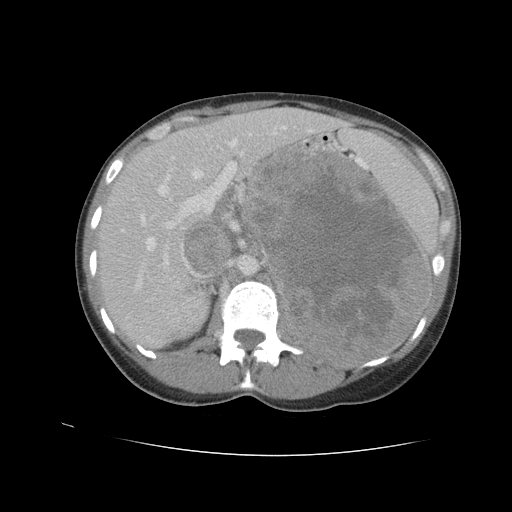
Contrast-enhanced abdominal CT, one axial slice; position 66 of 90 along the scan axis; intravenous contrast given; soft-tissue window (W 400 / L 40 HU); 5 mm slice thickness; 512 × 512 image matrix. Female patient. Case-level facts recorded for this patient, not image findings: diagnosis: adrenocortical carcinoma; tumour side: left adrenal; tumour size at pathology: 18 cm; Ki-67 index: 11 %; stage (as recorded): 3.
Annotated regions visible in this slice (semi-automatically segmented with operator editing):
- mass: bounding box [x1, y1, x2, y2] px = [248, 152, 430, 361]